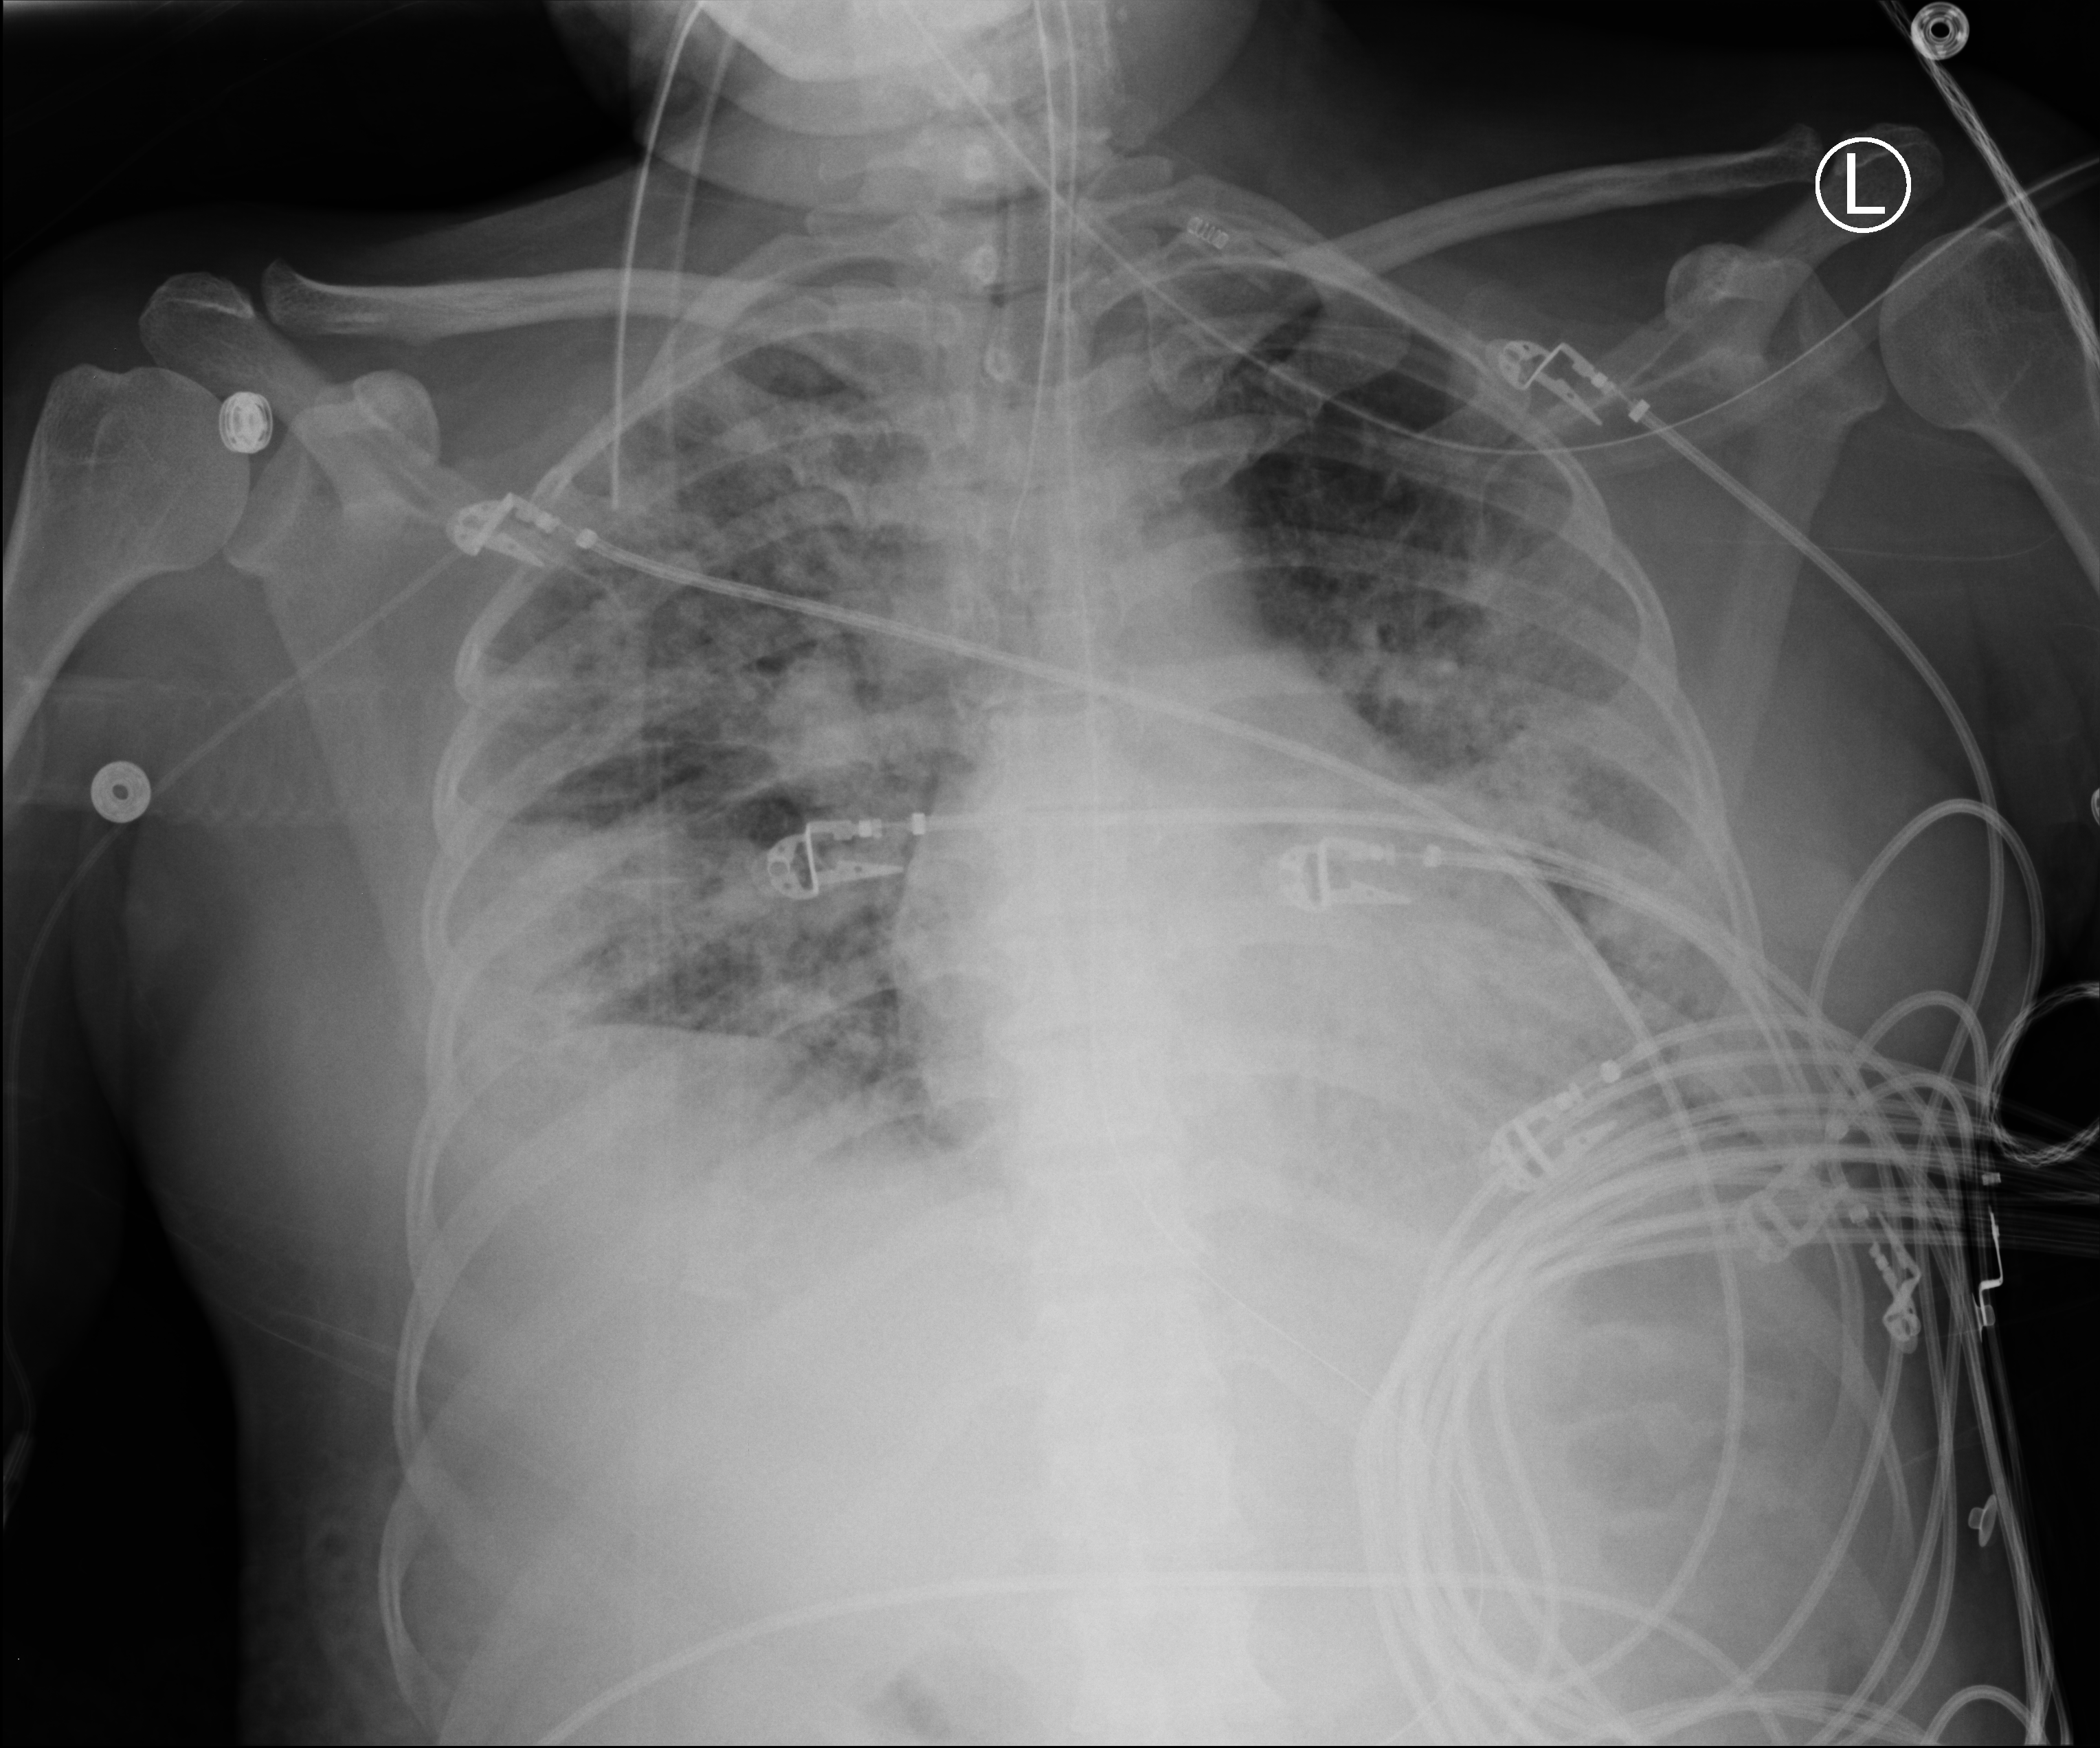
Bedside chest radiograph (computed radiography), anteroposterior (AP) projection. Patient hospitalised with COVID-19; female, aged 18–59 years.
Hospital-stay facts (about this admission, not read from this image; timing relative to this image not recorded):
- smoking status (admission record): former
- length of hospital stay: 71 days